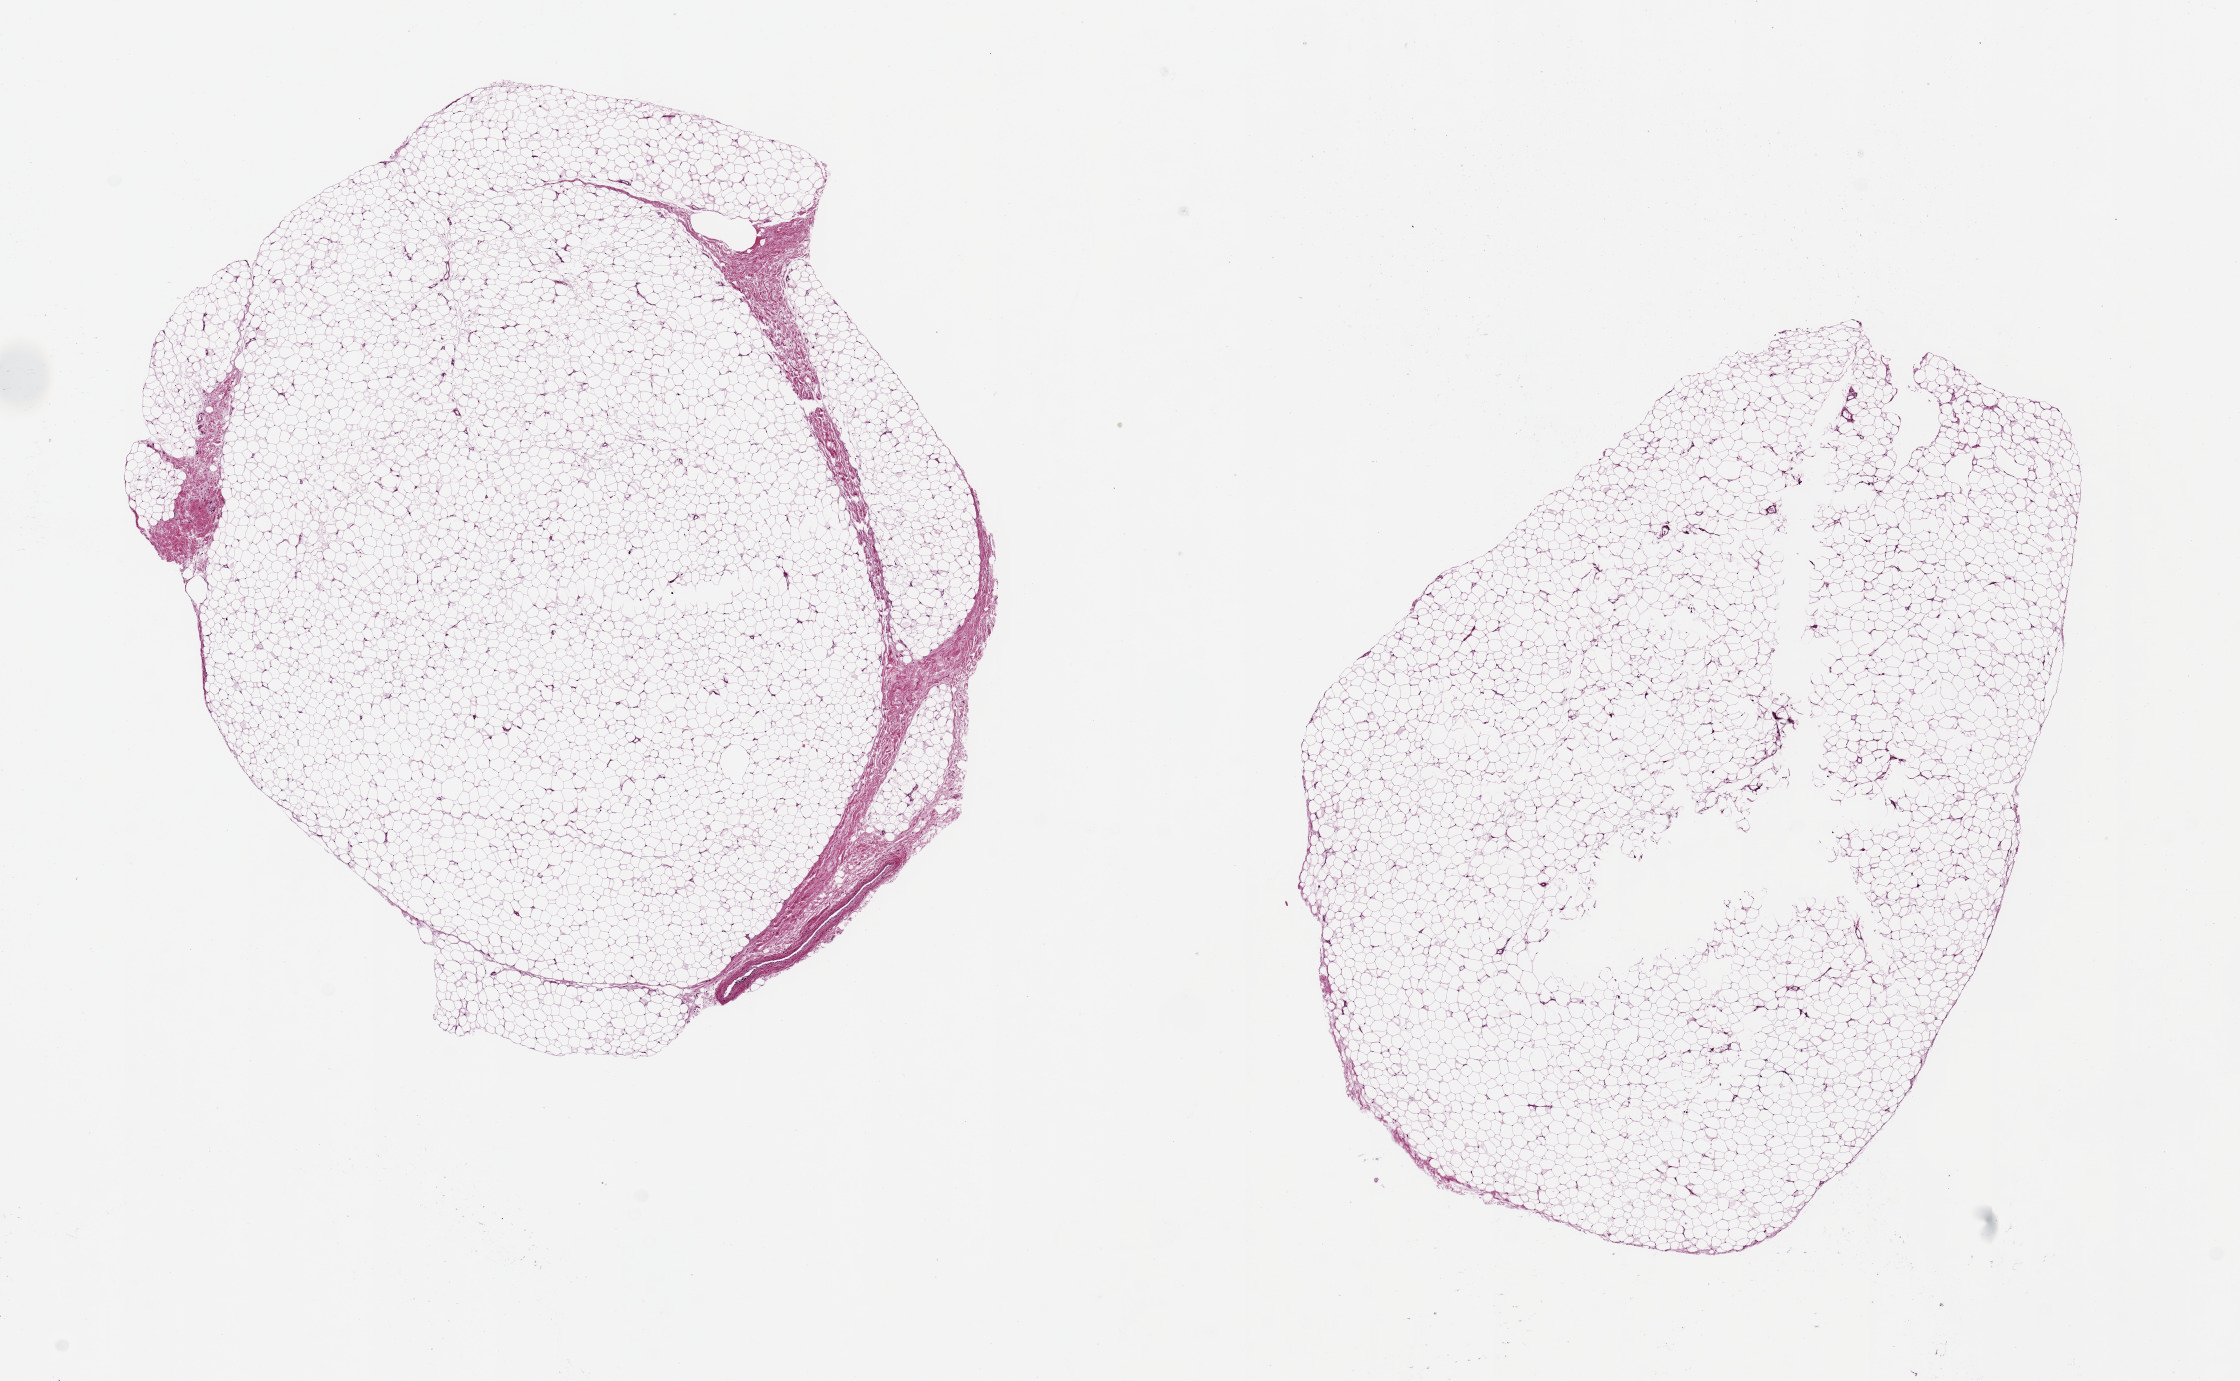
Haematoxylin and eosin whole-slide image, brightfield, shown as a low-resolution overview of the whole scanned area (about 17.7 x 10.9 mm, from a 20x scan), PAXgene-fixed, paraffin-embedded tissue, target tissue: adipose tissue, donor tissue sample. Donor sex: female.
Review note (as recorded): 2 pieces ~8x6mm.